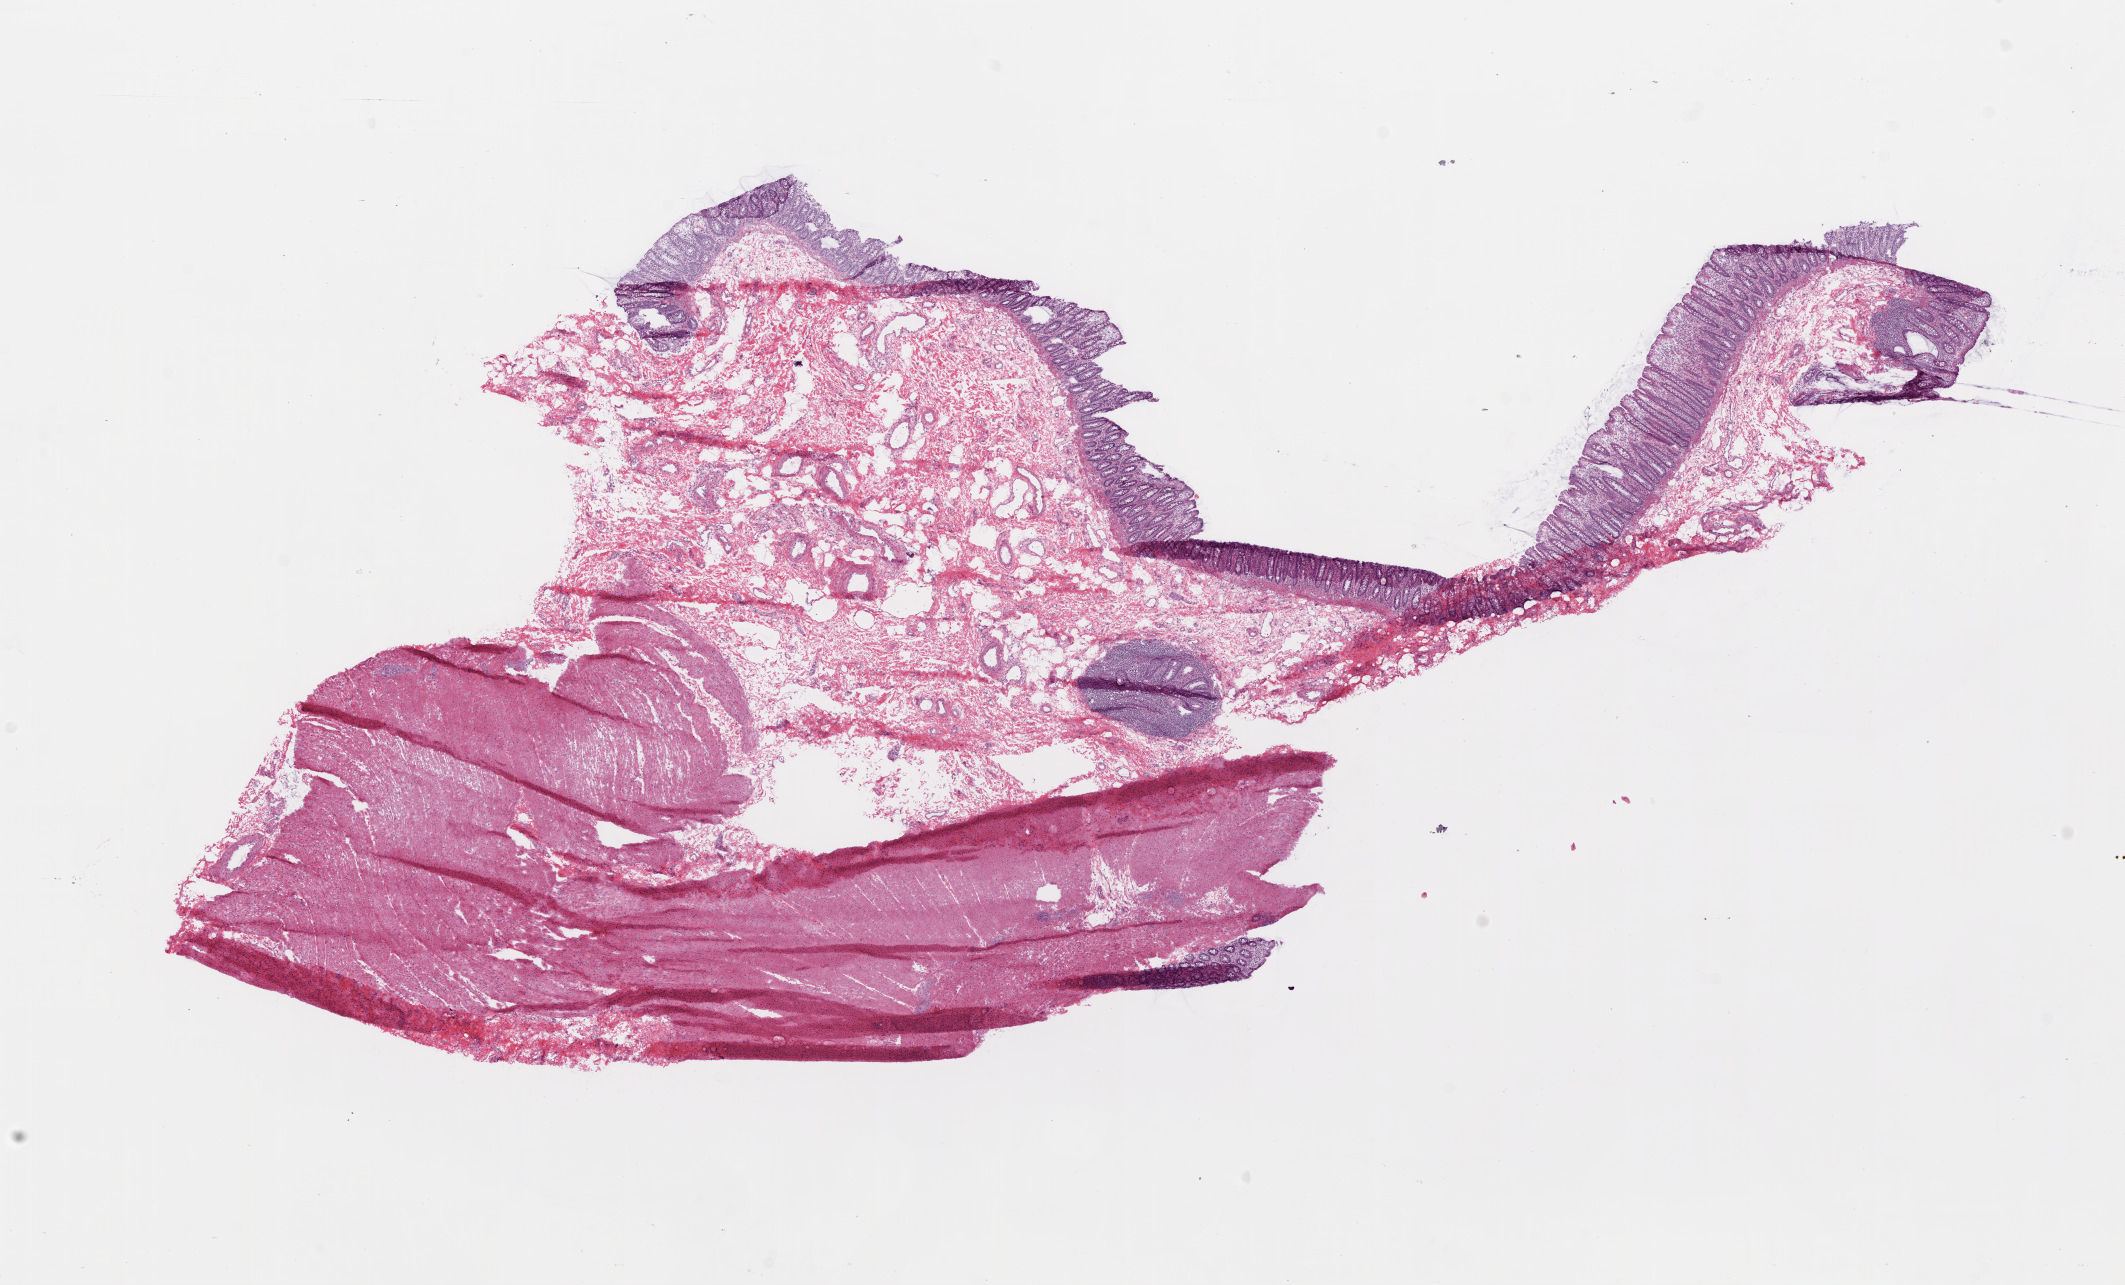
Whole-slide histology image, H&E-stained, whole scanned area (about 17.1 x 10.3 mm) shown as a low-resolution overview; frozen section from the bottom of the tissue portion; rectum, solid tissue normal (non-tumour tissue) sample. Patient: male, age at initial diagnosis 60 years.
This section: solid tissue normal (non-tumour) sample from the same patient. Patient diagnosis: Adenocarcinoma, NOS (rectosigmoid junction).